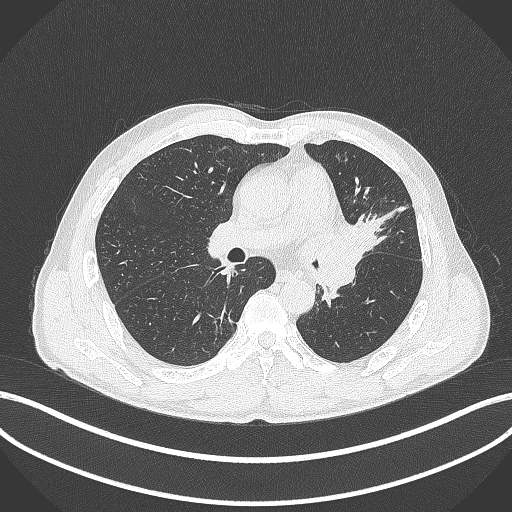
Chest CT, one axial slice; slice 235 of 429 in the series (ordered by position); reconstruction kernel B70f; lung window (W 1500 / L -600 HU); 1 mm slice thickness; 512 × 512 image matrix, field of view 400 × 400 mm. Male patient, age 57 years. From the clinical record (not read from this slice): clinical TNM (as recorded): T2b N0 M0.
Outlined on this slice (bounding box drawn by a radiologist):
- lung tumour (recorded histology: squamous cell carcinoma): bounding box (x1, y1, x2, y2) in pixels: (329, 217, 379, 266)